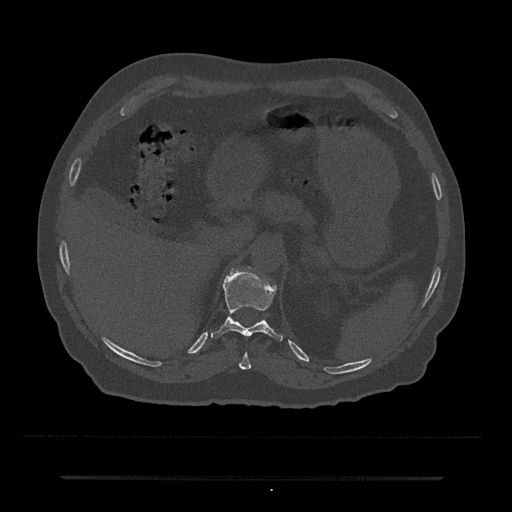
CT including the spine, one axial slice; position 181 of 797 along the scan axis; reconstruction kernel Br40s/3; bone window (W 1800 / L 400 HU); 0.5 mm slice thickness; 512 × 512 image matrix, field of view 437 × 437 mm. Patient: male, 69 years. From the clinical record (not read from this slice): primary cancer: prostate.
Annotated regions visible in this slice (semi-automatic segmentation, software-assisted and operator-edited):
- T10 vertebra: bounding box [x1, y1, x2, y2] px = [239, 352, 251, 370]
- T11 vertebra: [211, 271, 283, 342]